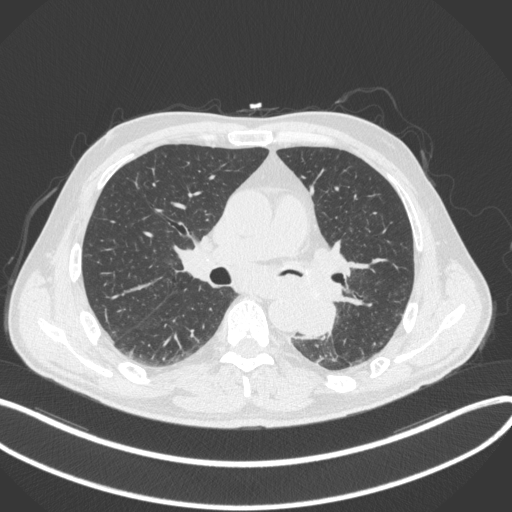
Chest CT, one axial slice; slice 197 of 328 in the series (ordered by position); reconstruction kernel B31f; lung window (W 1500 / L -600 HU); 512 × 512 image matrix. Male patient, age 59 years. From the clinical record (not read from this slice): clinical TNM (as recorded): T2a N2 M0.
Structures marked on this image (bounding box drawn by a radiologist):
- lung tumour (recorded histology: squamous cell carcinoma): bounding box [x1, y1, x2, y2] px = [297, 289, 339, 344]